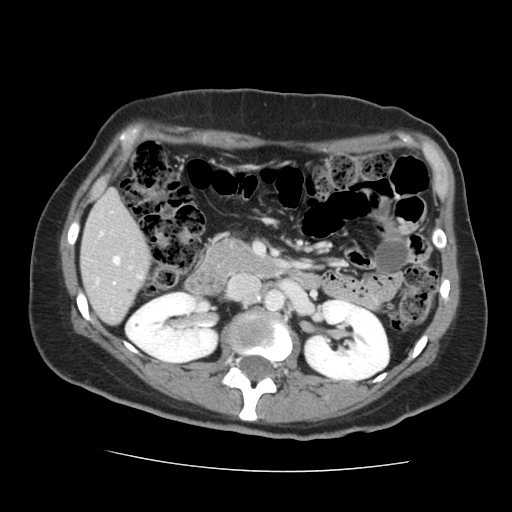
Contrast-enhanced abdominal CT, one axial slice; slice 64 of 144 in the series (ordered by position); 120 kVp; intravenous contrast given; soft-tissue window (W 400 / L 40 HU); 2.5 mm slice thickness; 512 × 512 image matrix, field of view 333 × 333 mm. Female patient, age 46 years. Case-level facts recorded for this patient, not image findings: diagnosis: colorectal cancer liver metastases, imaged before liver resection; multiple liver metastases: no; largest metastasis: 2.8 cm; chemotherapy before resection: yes.
Annotated regions visible in this slice (outlined manually by an expert reader):
- liver: box from (x=82, y=193) to (x=148, y=323) px
- planned liver remnant (the part of the liver to remain after resection): (x=82, y=193)–(x=148, y=323)
- portal vein (with intrahepatic branches): (x=113, y=258)–(x=119, y=264)